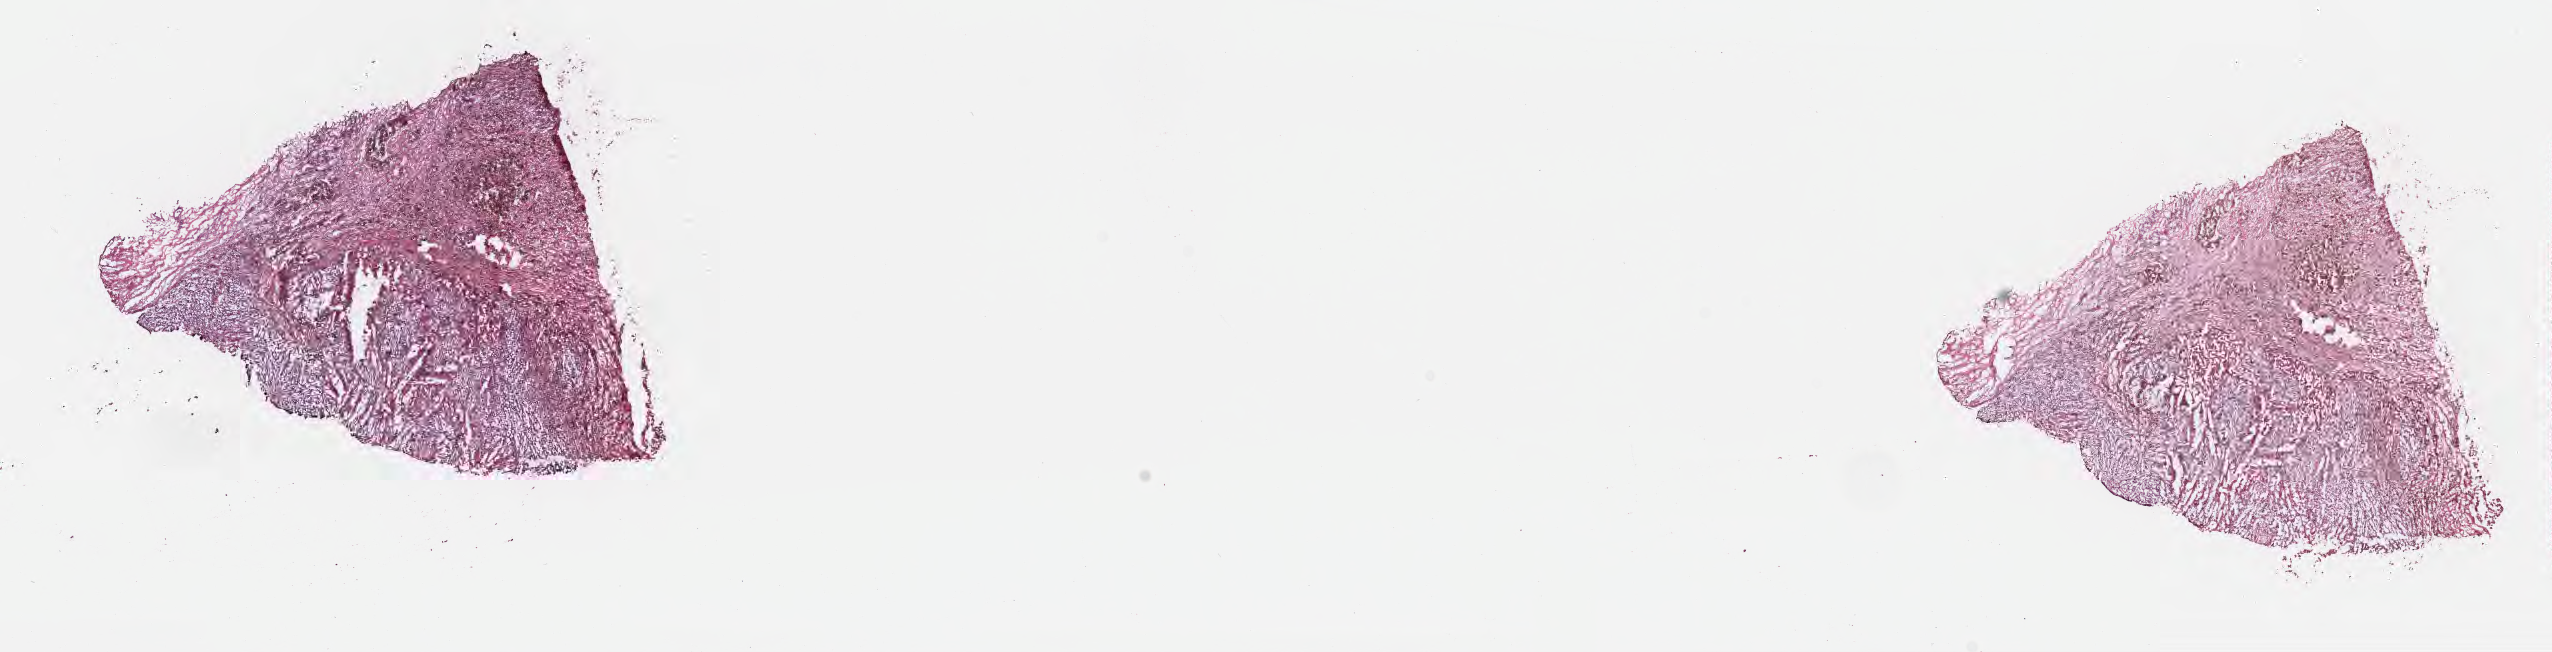
H&E whole-slide image — low-resolution overview of the scanned area, about 20.6 x 5.3 mm. Cryosection. Metastatic tumor tissue, resected from lymph nodes of inguinal region or leg. Patient: female, age at initial diagnosis 45 years. Slide review estimates, as recorded: tumor cells 35%, tumor nuclei 60%, stromal cells 0%, necrosis 10%, normal cells 55%. Inflammatory infiltration, as recorded: lymphocyte infiltration 0%, monocyte infiltration 0%, neutrophil infiltration 0%.
Patient diagnosis (primary): Malignant melanoma, NOS. Section: top of the tissue portion.